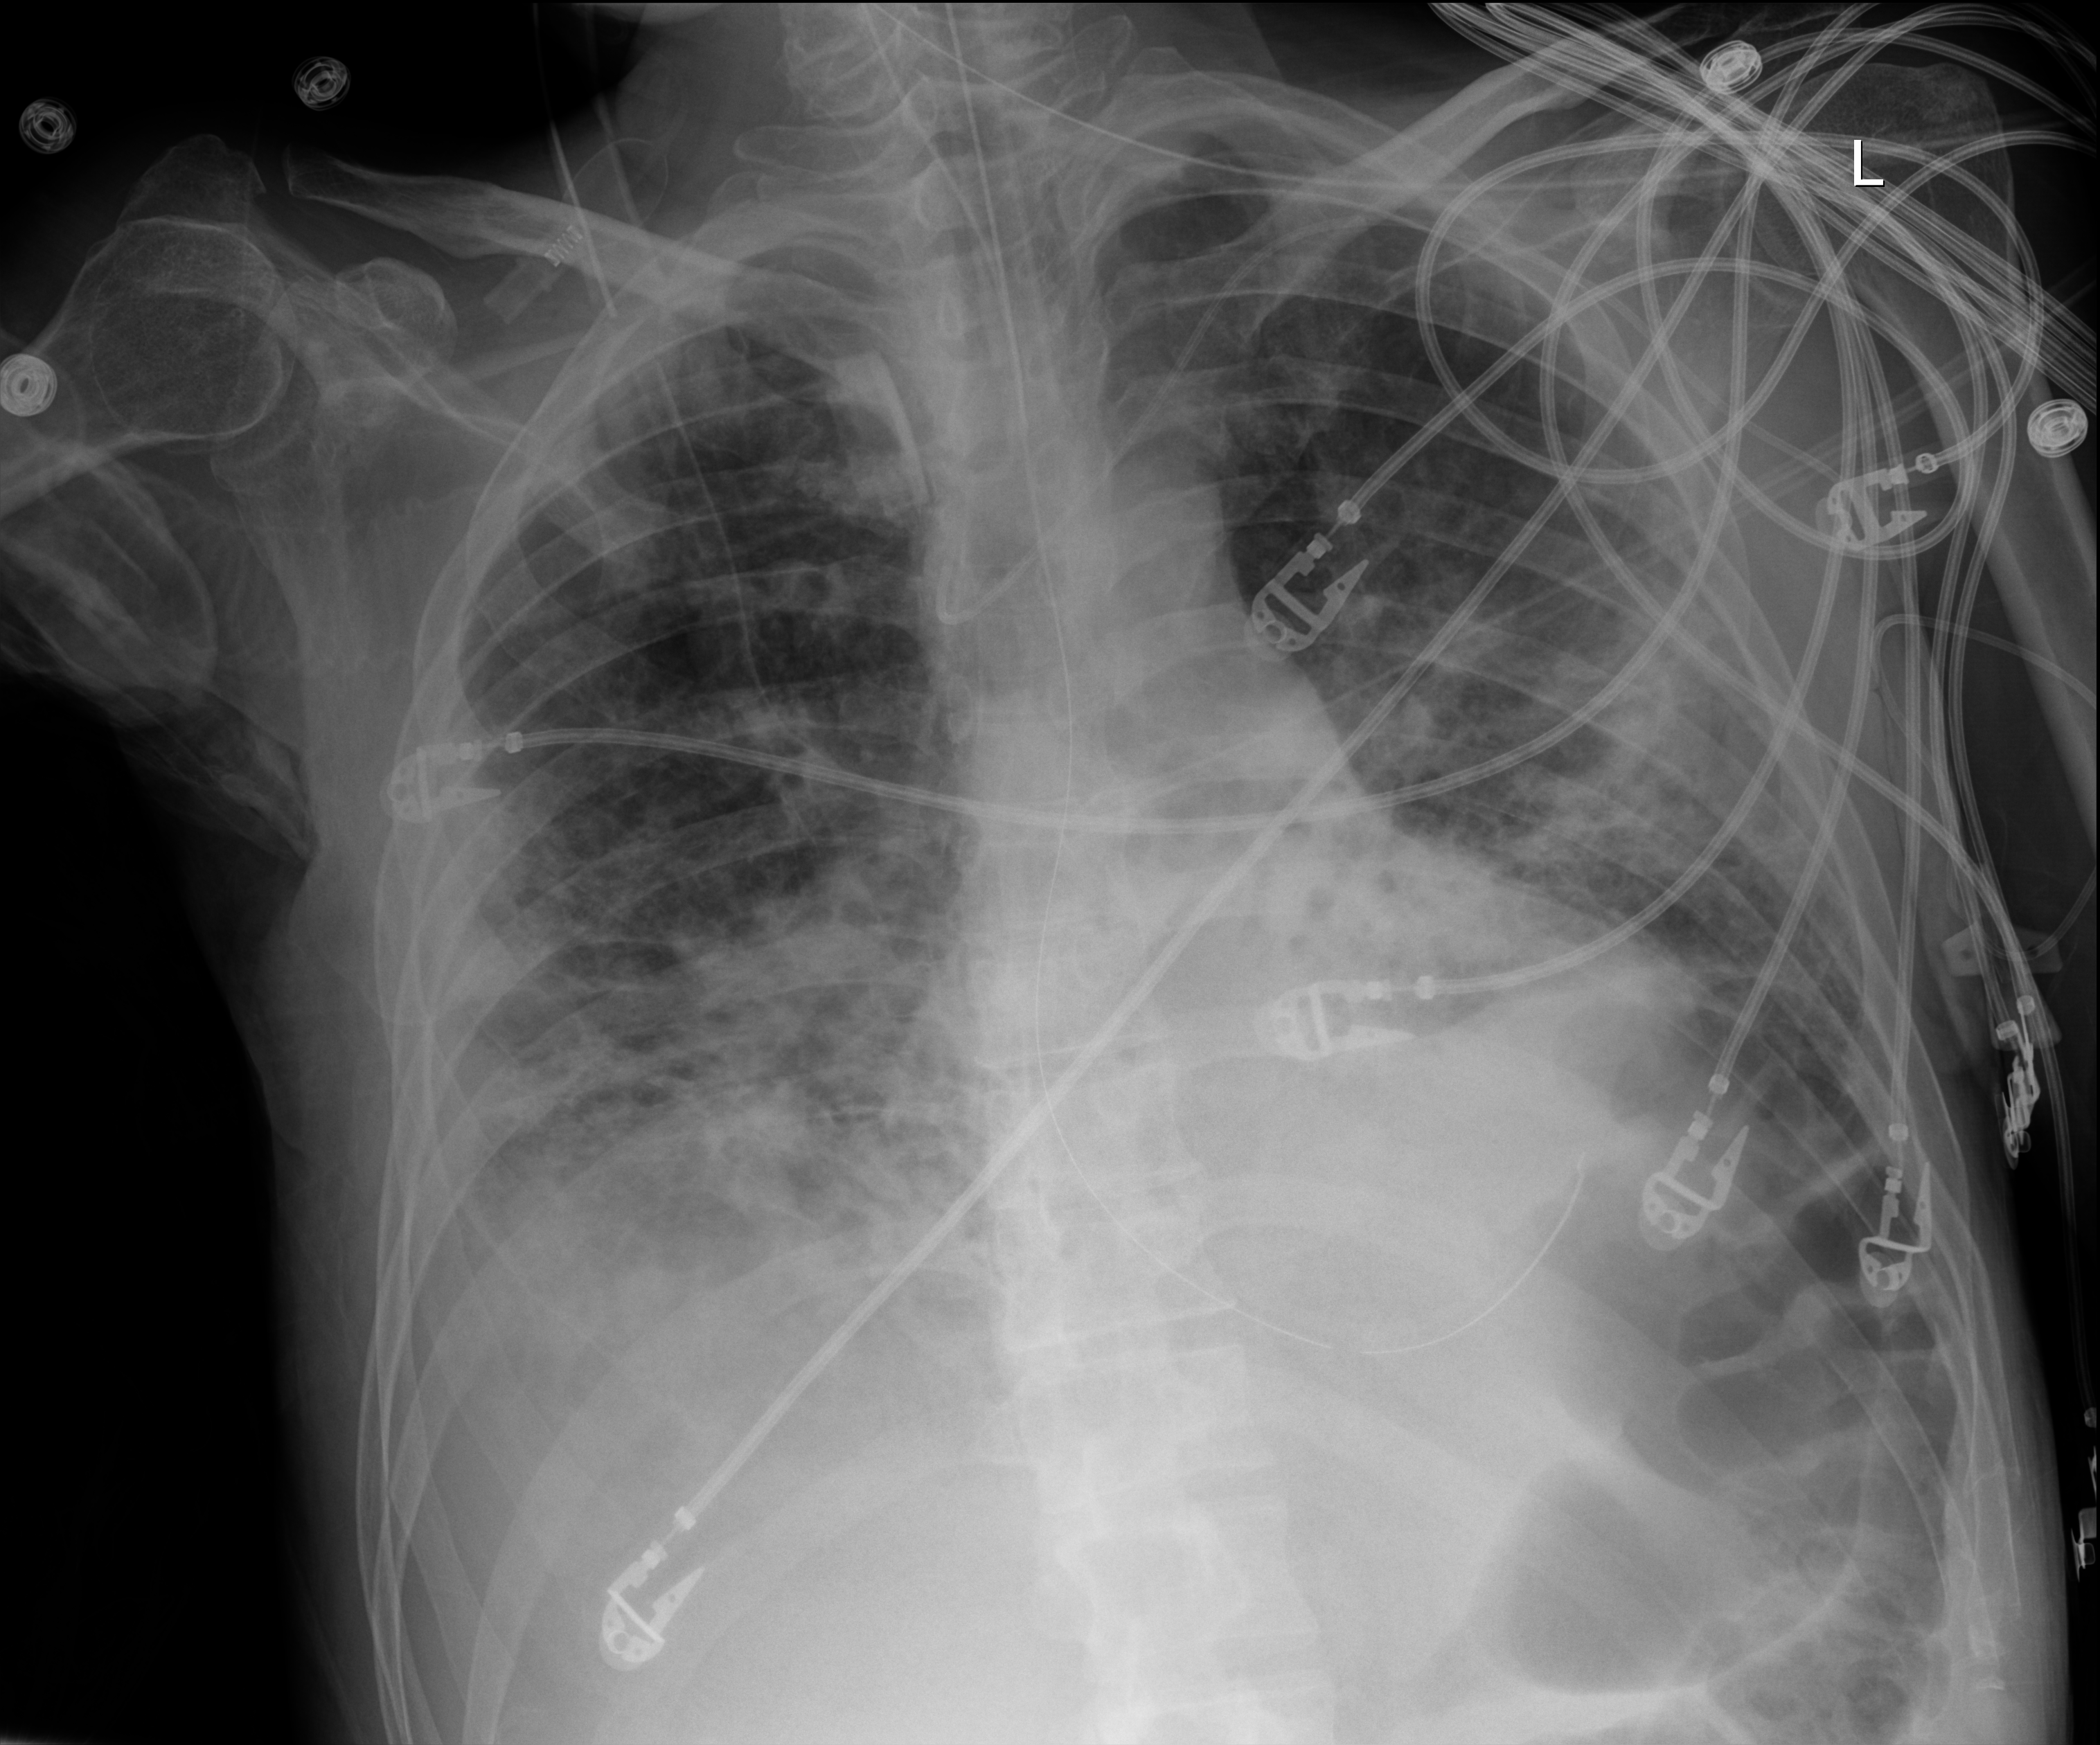
Bedside chest radiograph (digital radiography), anteroposterior (AP) projection. Patient hospitalised with COVID-19; male, aged 18–59 years.
Admission-level facts for this patient (not findings on this image; timing relative to this image not recorded): diabetes (admission record): yes; hypertension (admission record): yes; admitted to intensive care during this hospital stay: yes.